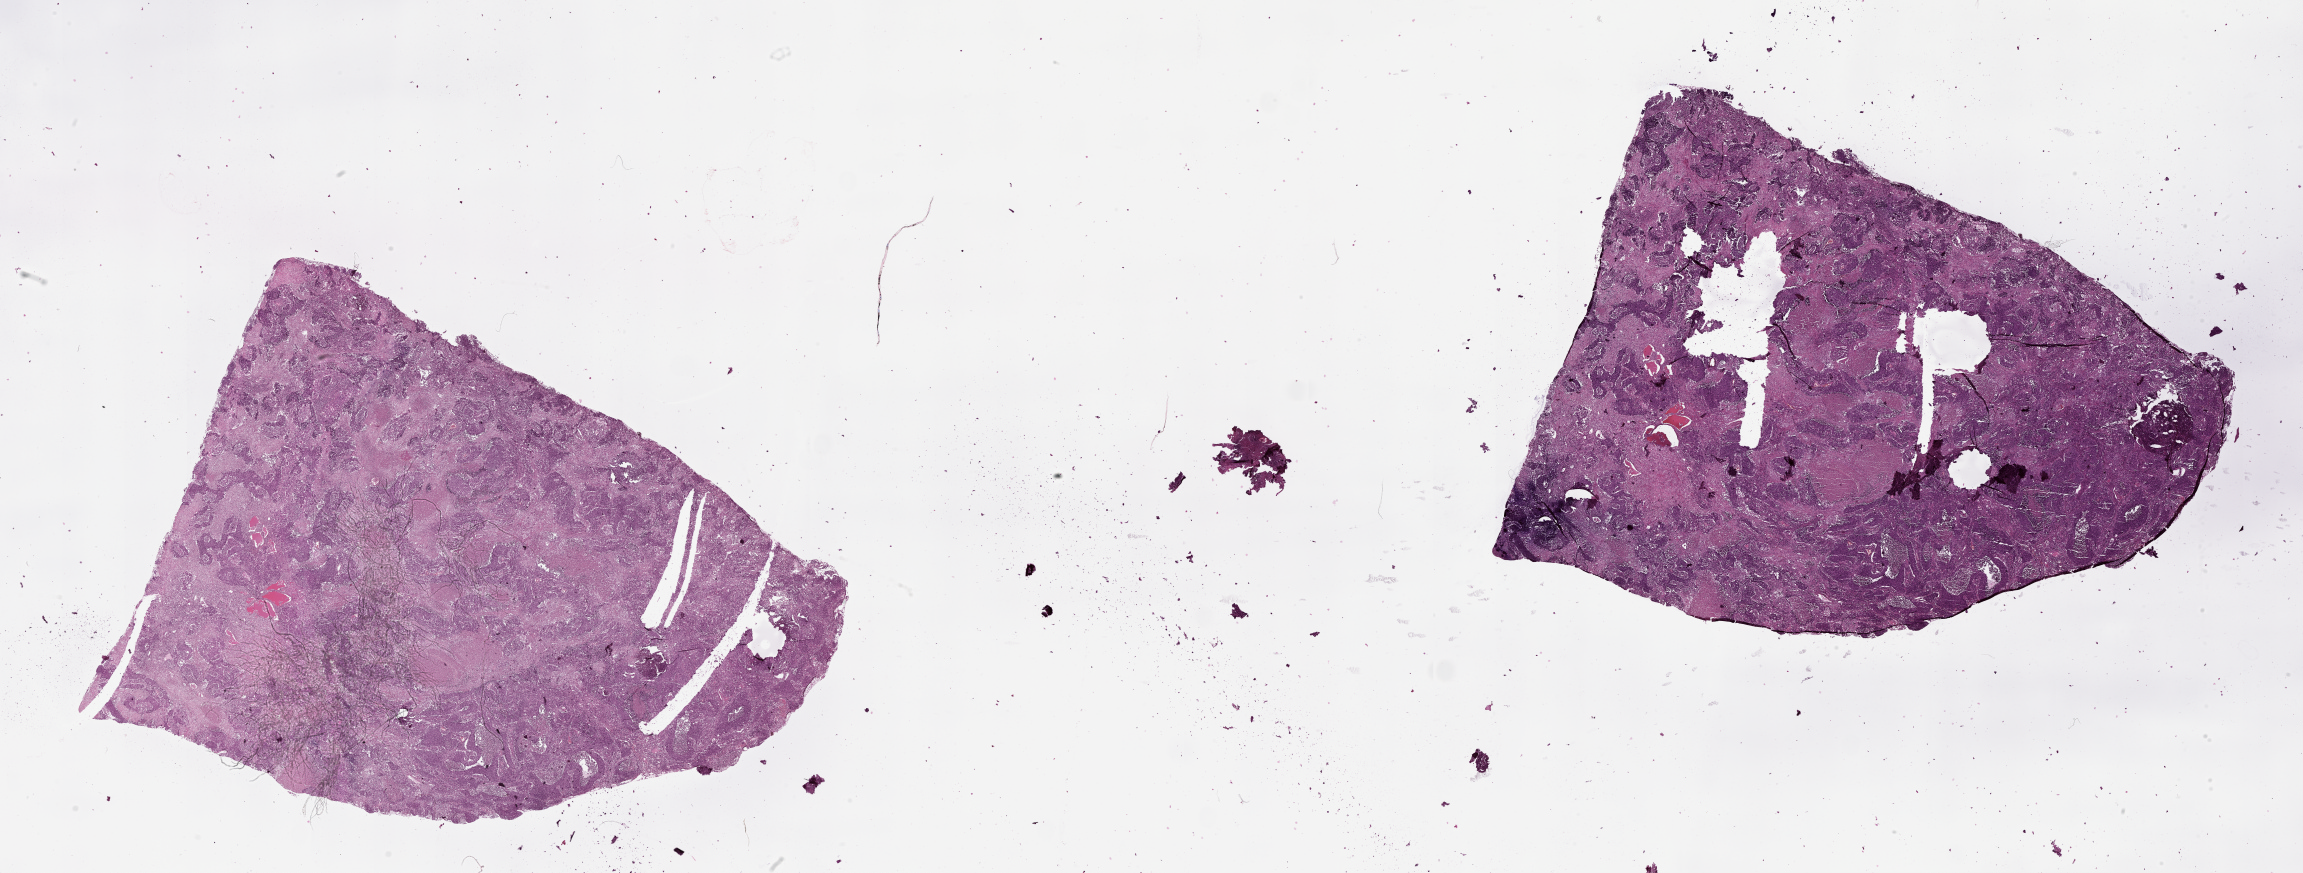
Whole-slide histology image, Hematoxylin and eosin (H&E) stained — whole scanned area (about 37.1 x 14.1 mm, acquisition: 20x scan) shown as a low-resolution overview; tumour tissue sample, lung. 68-year-old male patient.
Patient diagnosis (cohort enrolment): squamous cell carcinoma (lung).